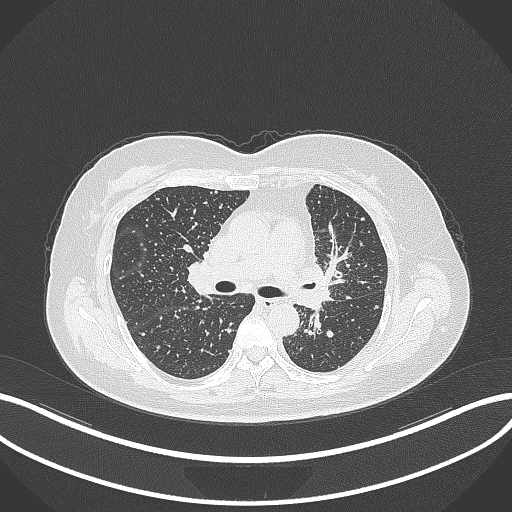
Chest CT, one axial slice; position 203 of 348 along the scan axis; 120 kVp; lung window (W 1500 / L -600 HU); 1 mm slice thickness; 512 × 512 image matrix, field of view 400 × 400 mm. Patient: female, 49 years. From the clinical record (not read from this slice): clinical TNM (as recorded): T1c N0 M1.
Structures marked on this image (rectangle marked by the reading radiologist):
- lung tumour (recorded histology: adenocarcinoma): bounding box (x1, y1, x2, y2) in pixels: (288, 258, 338, 311)